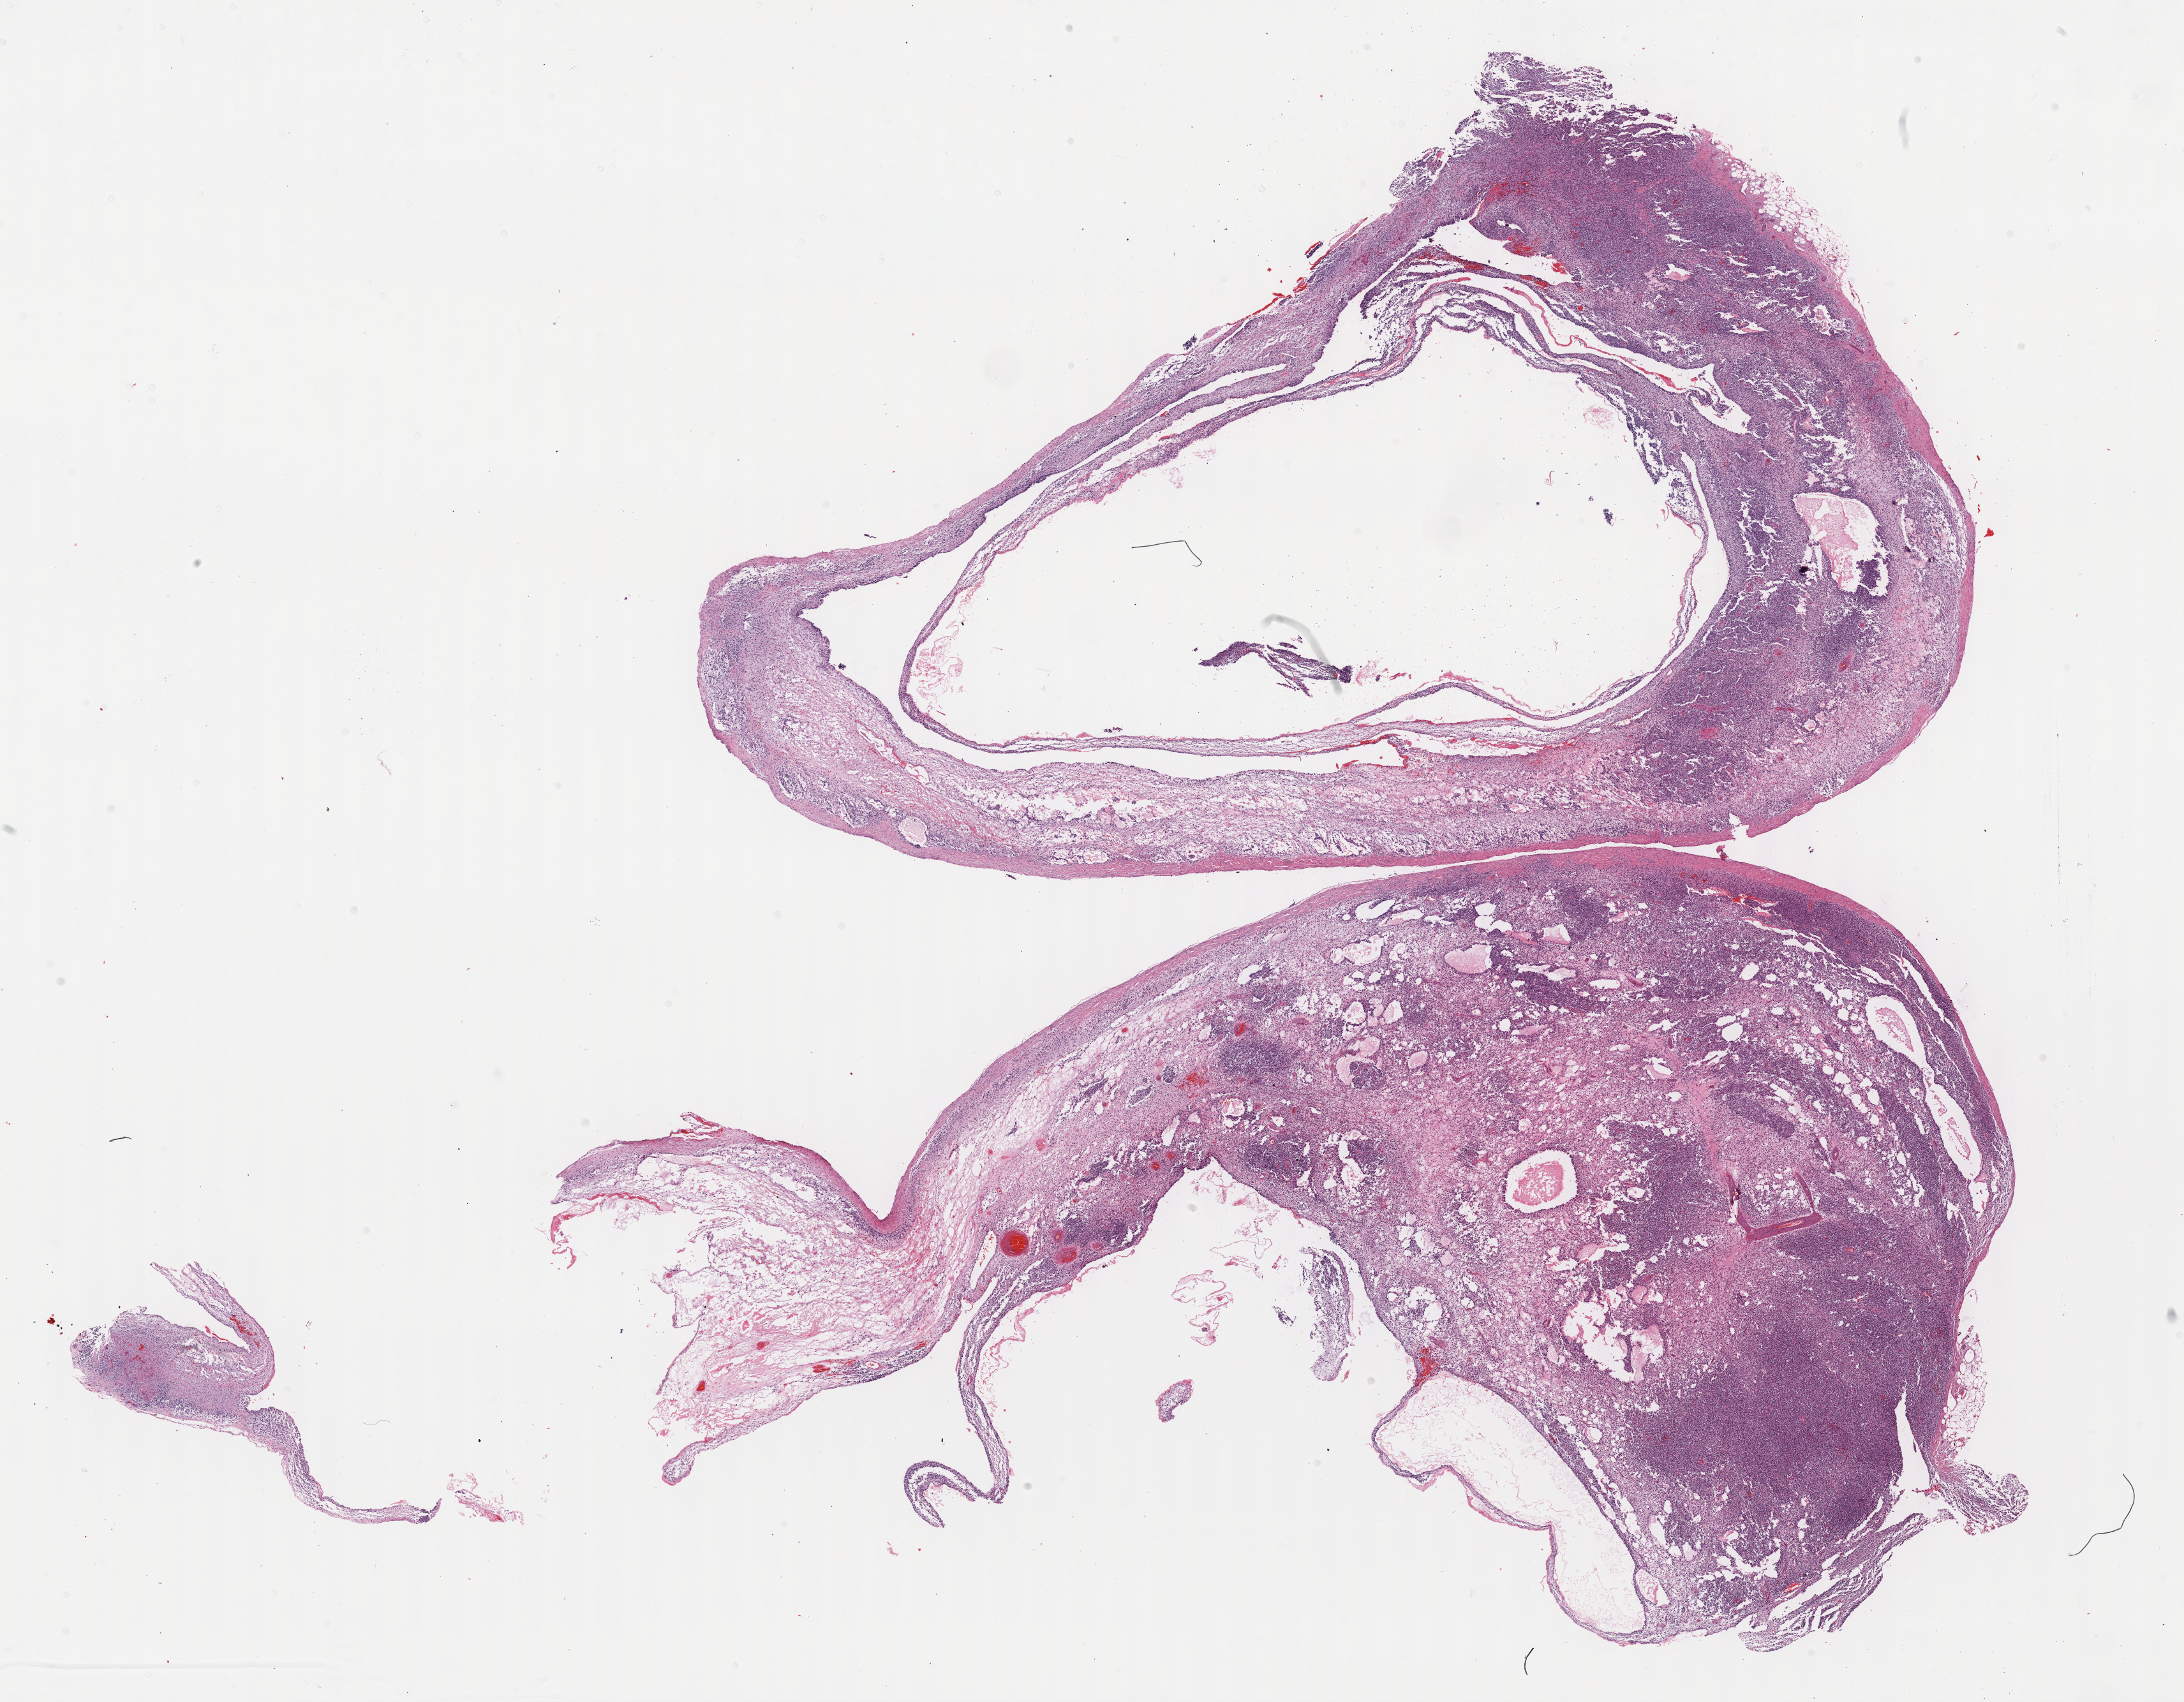
H&E whole-slide image — low-resolution overview of the scanned area, about 27.7 x 21.6 mm (from a 40x scan), FFPE section, primary tumour sample from the retroperitoneum and peritoneum. Patient: male, age at initial diagnosis 57 years.
• diagnosis: Dedifferentiated liposarcoma (retroperitoneum)